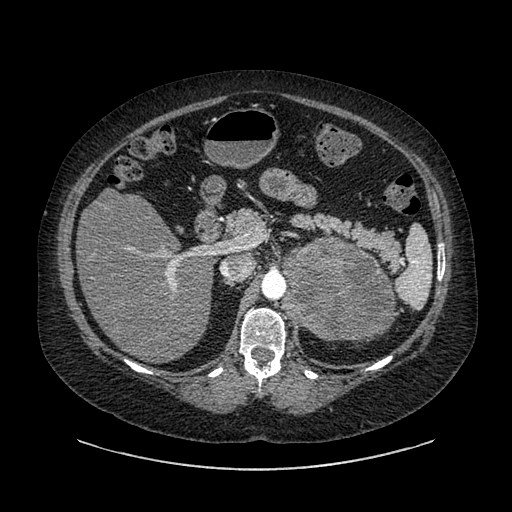
Contrast-enhanced abdominal CT, one axial slice. Reconstruction kernel SOFT. 120 kVp. Intravenous contrast given. Soft-tissue window (W 400 / L 40 HU). 0.62 mm slice thickness. 512 × 512 image matrix. Female patient, age 61 years. Case-level facts recorded for this patient, not image findings: diagnosis: adrenocortical carcinoma; tumour side: left adrenal; tumour size at pathology: 13 cm; Ki-67 index: 79 %; stage (as recorded): 2.
Outlined on this slice (semi-automatically segmented with operator editing):
- mass: bounding box <282,235,394,341> (left, top, right, bottom; pixels)